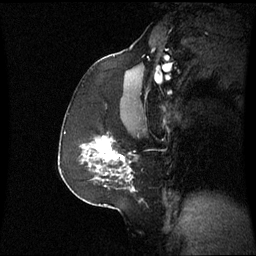
Breast MRI (dynamic contrast-enhanced), one sagittal slice. Slice 38 of 60 in the series (ordered by position). Dynamic contrast-enhanced series, image 2 of 3 at this slice position (ordered by acquisition). 1.5 T. TE 4.2 ms, TR 8.9 ms. 2.4 mm slice thickness. 256 × 256 image matrix, field of view 230 × 230 mm. Patient: female, 59 years. Case-level facts recorded for this patient, not image findings: setting: breast cancer imaged before/during neoadjuvant chemotherapy; receptor status: triple-negative.
Structures marked on this image (semi-automatic segmentation, software-assisted and operator-edited):
- analysis volume of interest (the breast-tissue region the enhancement analysis was run in; not a lesion): box from (x=86, y=136) to (x=138, y=182) px
- tumour enhancement mask (voxels above the 70 % enhancement threshold inside the analysis volume of interest): (x=96, y=138)–(x=131, y=172)